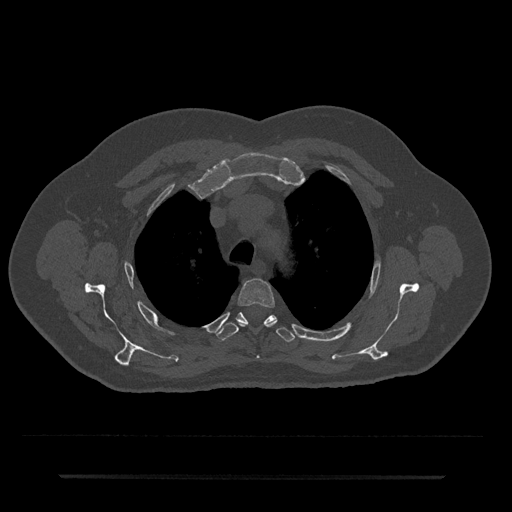
CT including the spine, one axial slice; slice 550 of 797 in the series (ordered by position); 120 kVp; bone window (W 1800 / L 400 HU); 512 × 512 image matrix. Patient: male, 69 years. From the clinical record (not read from this slice): primary cancer: prostate.
Structures marked on this image (semi-automatically segmented with operator editing):
- T3 vertebra: box from (x=236, y=279) to (x=277, y=358) px
- T4 vertebra: (x=216, y=312)–(x=295, y=342)